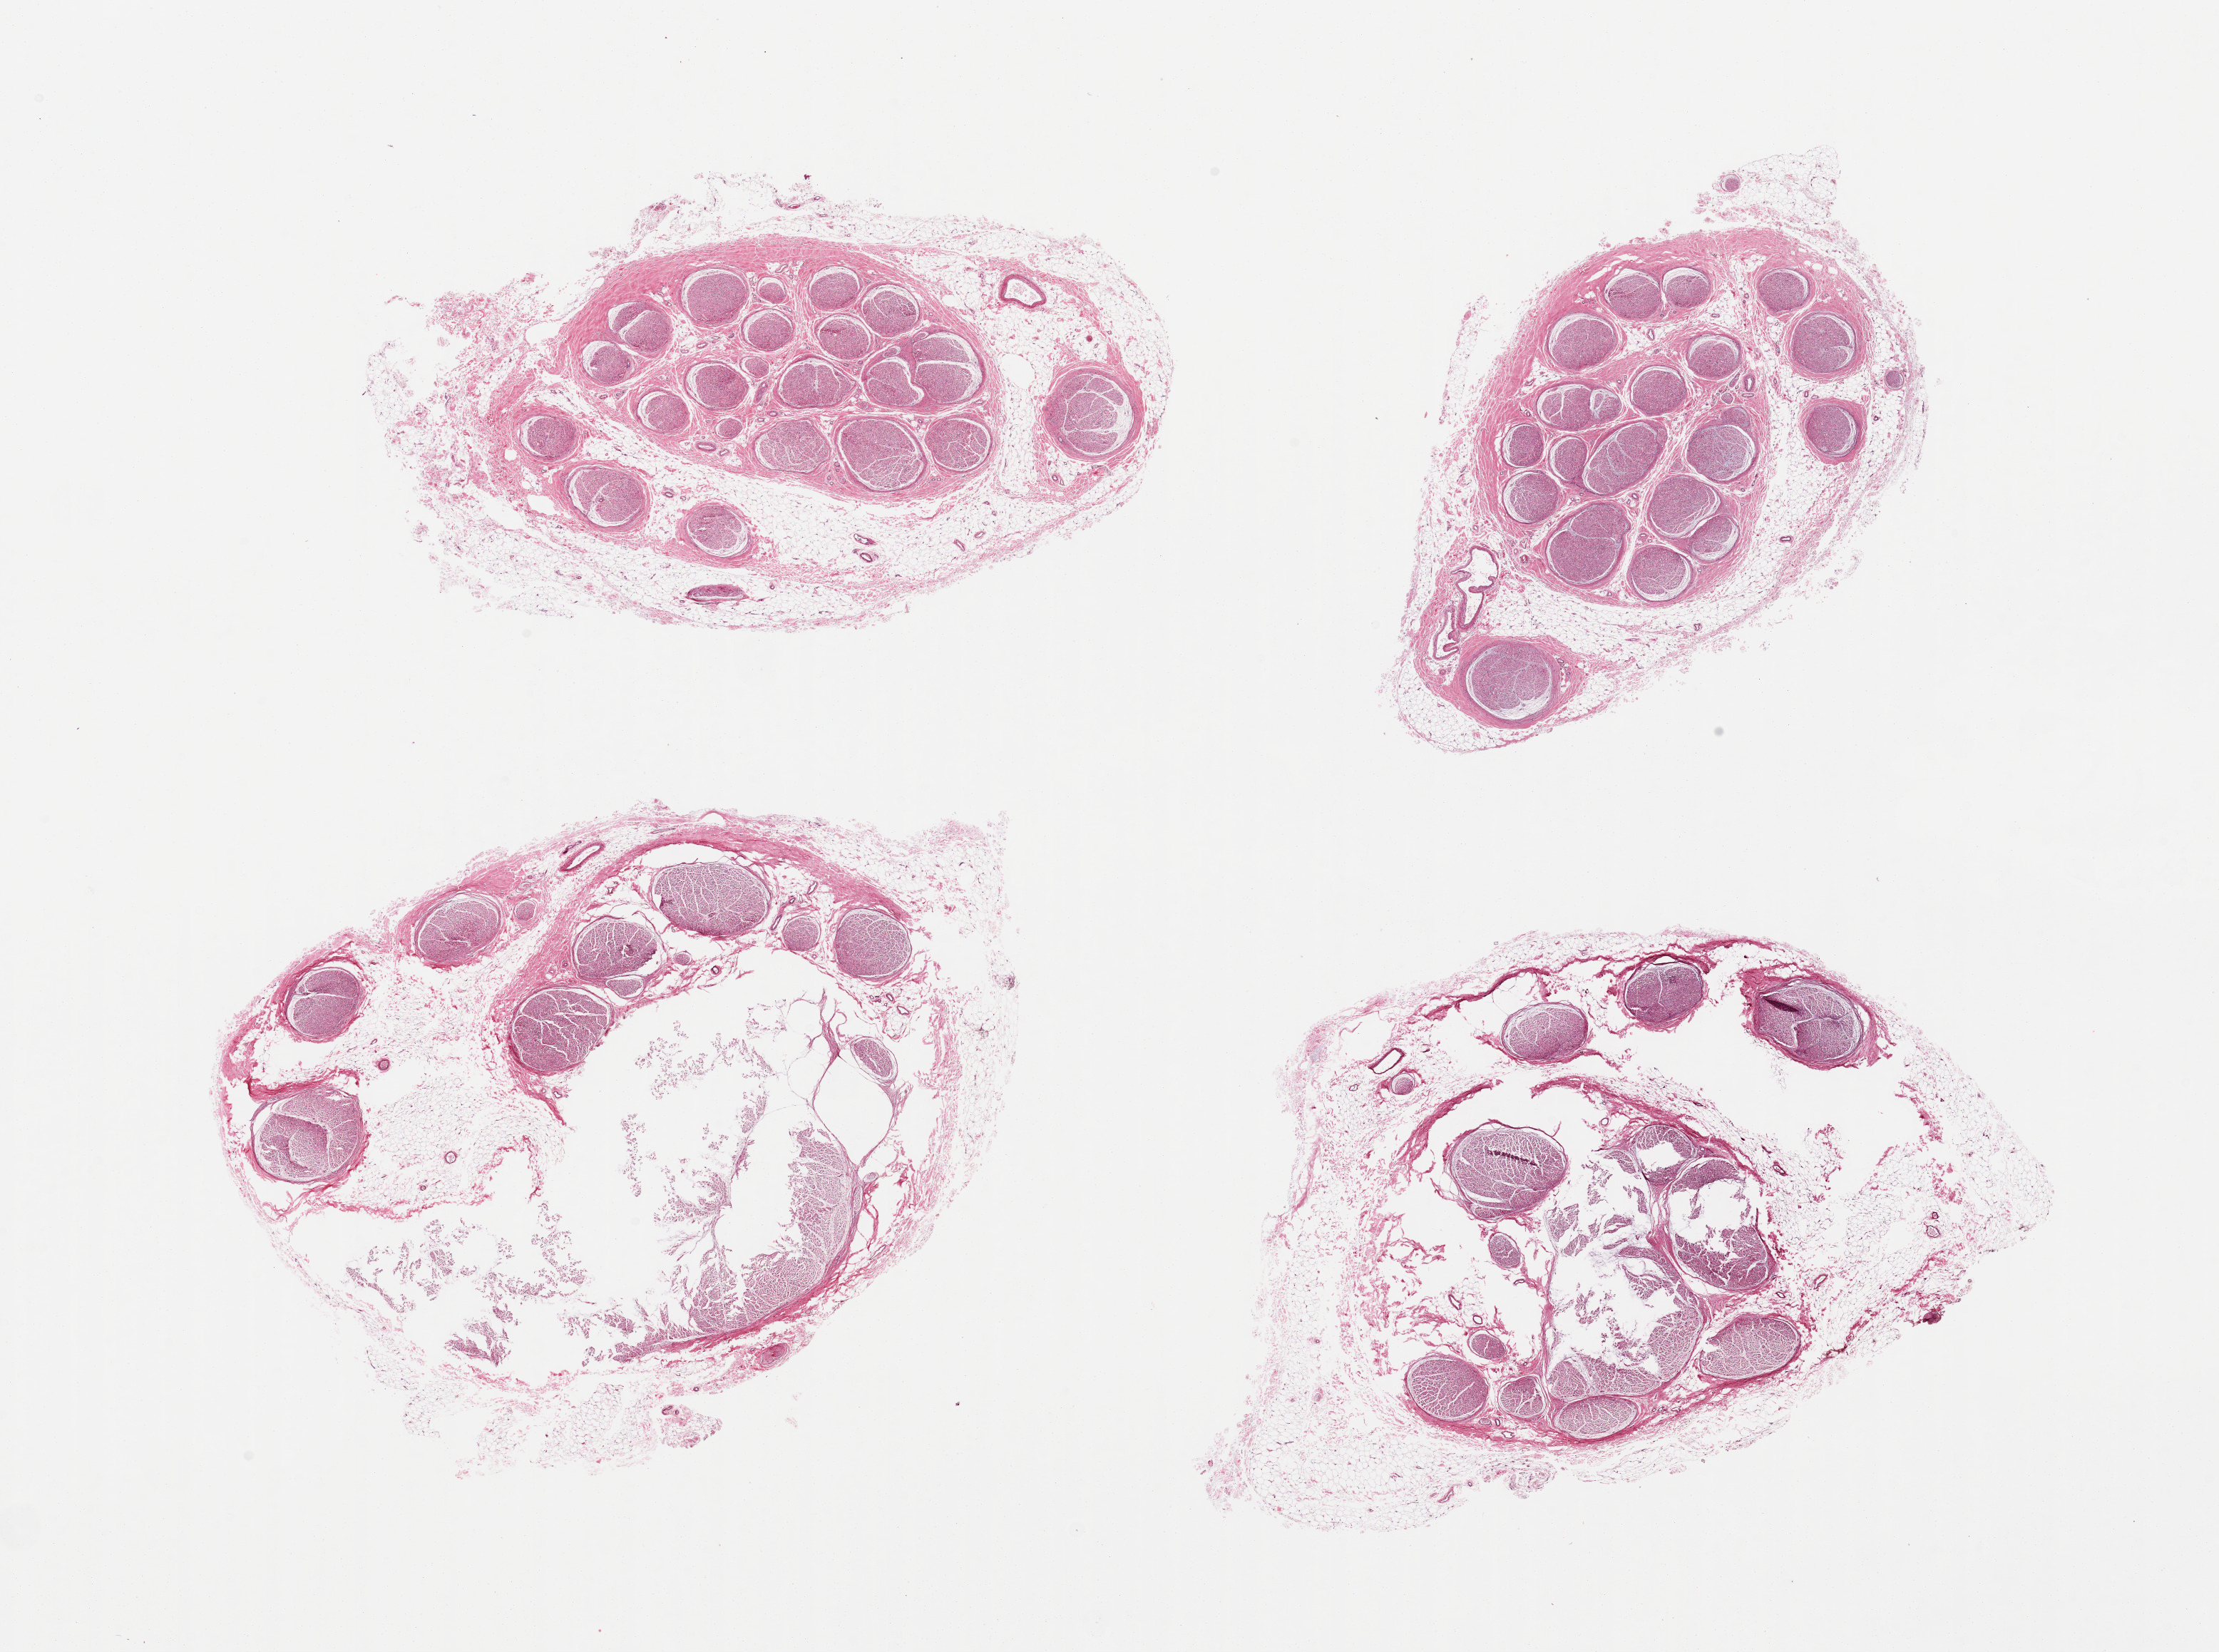
H&E whole-slide image, brightfield — low-resolution overview of the scanned area, about 24.6 x 18.3 mm; PAXgene-fixed, paraffin-embedded tissue; sampled site (target tissue): tibial nerve; donor tissue sample. Male donor.
Reviewer comment on this tissue sample: 4 pieces, 2 not intact, all with residual attached adipose tissue.